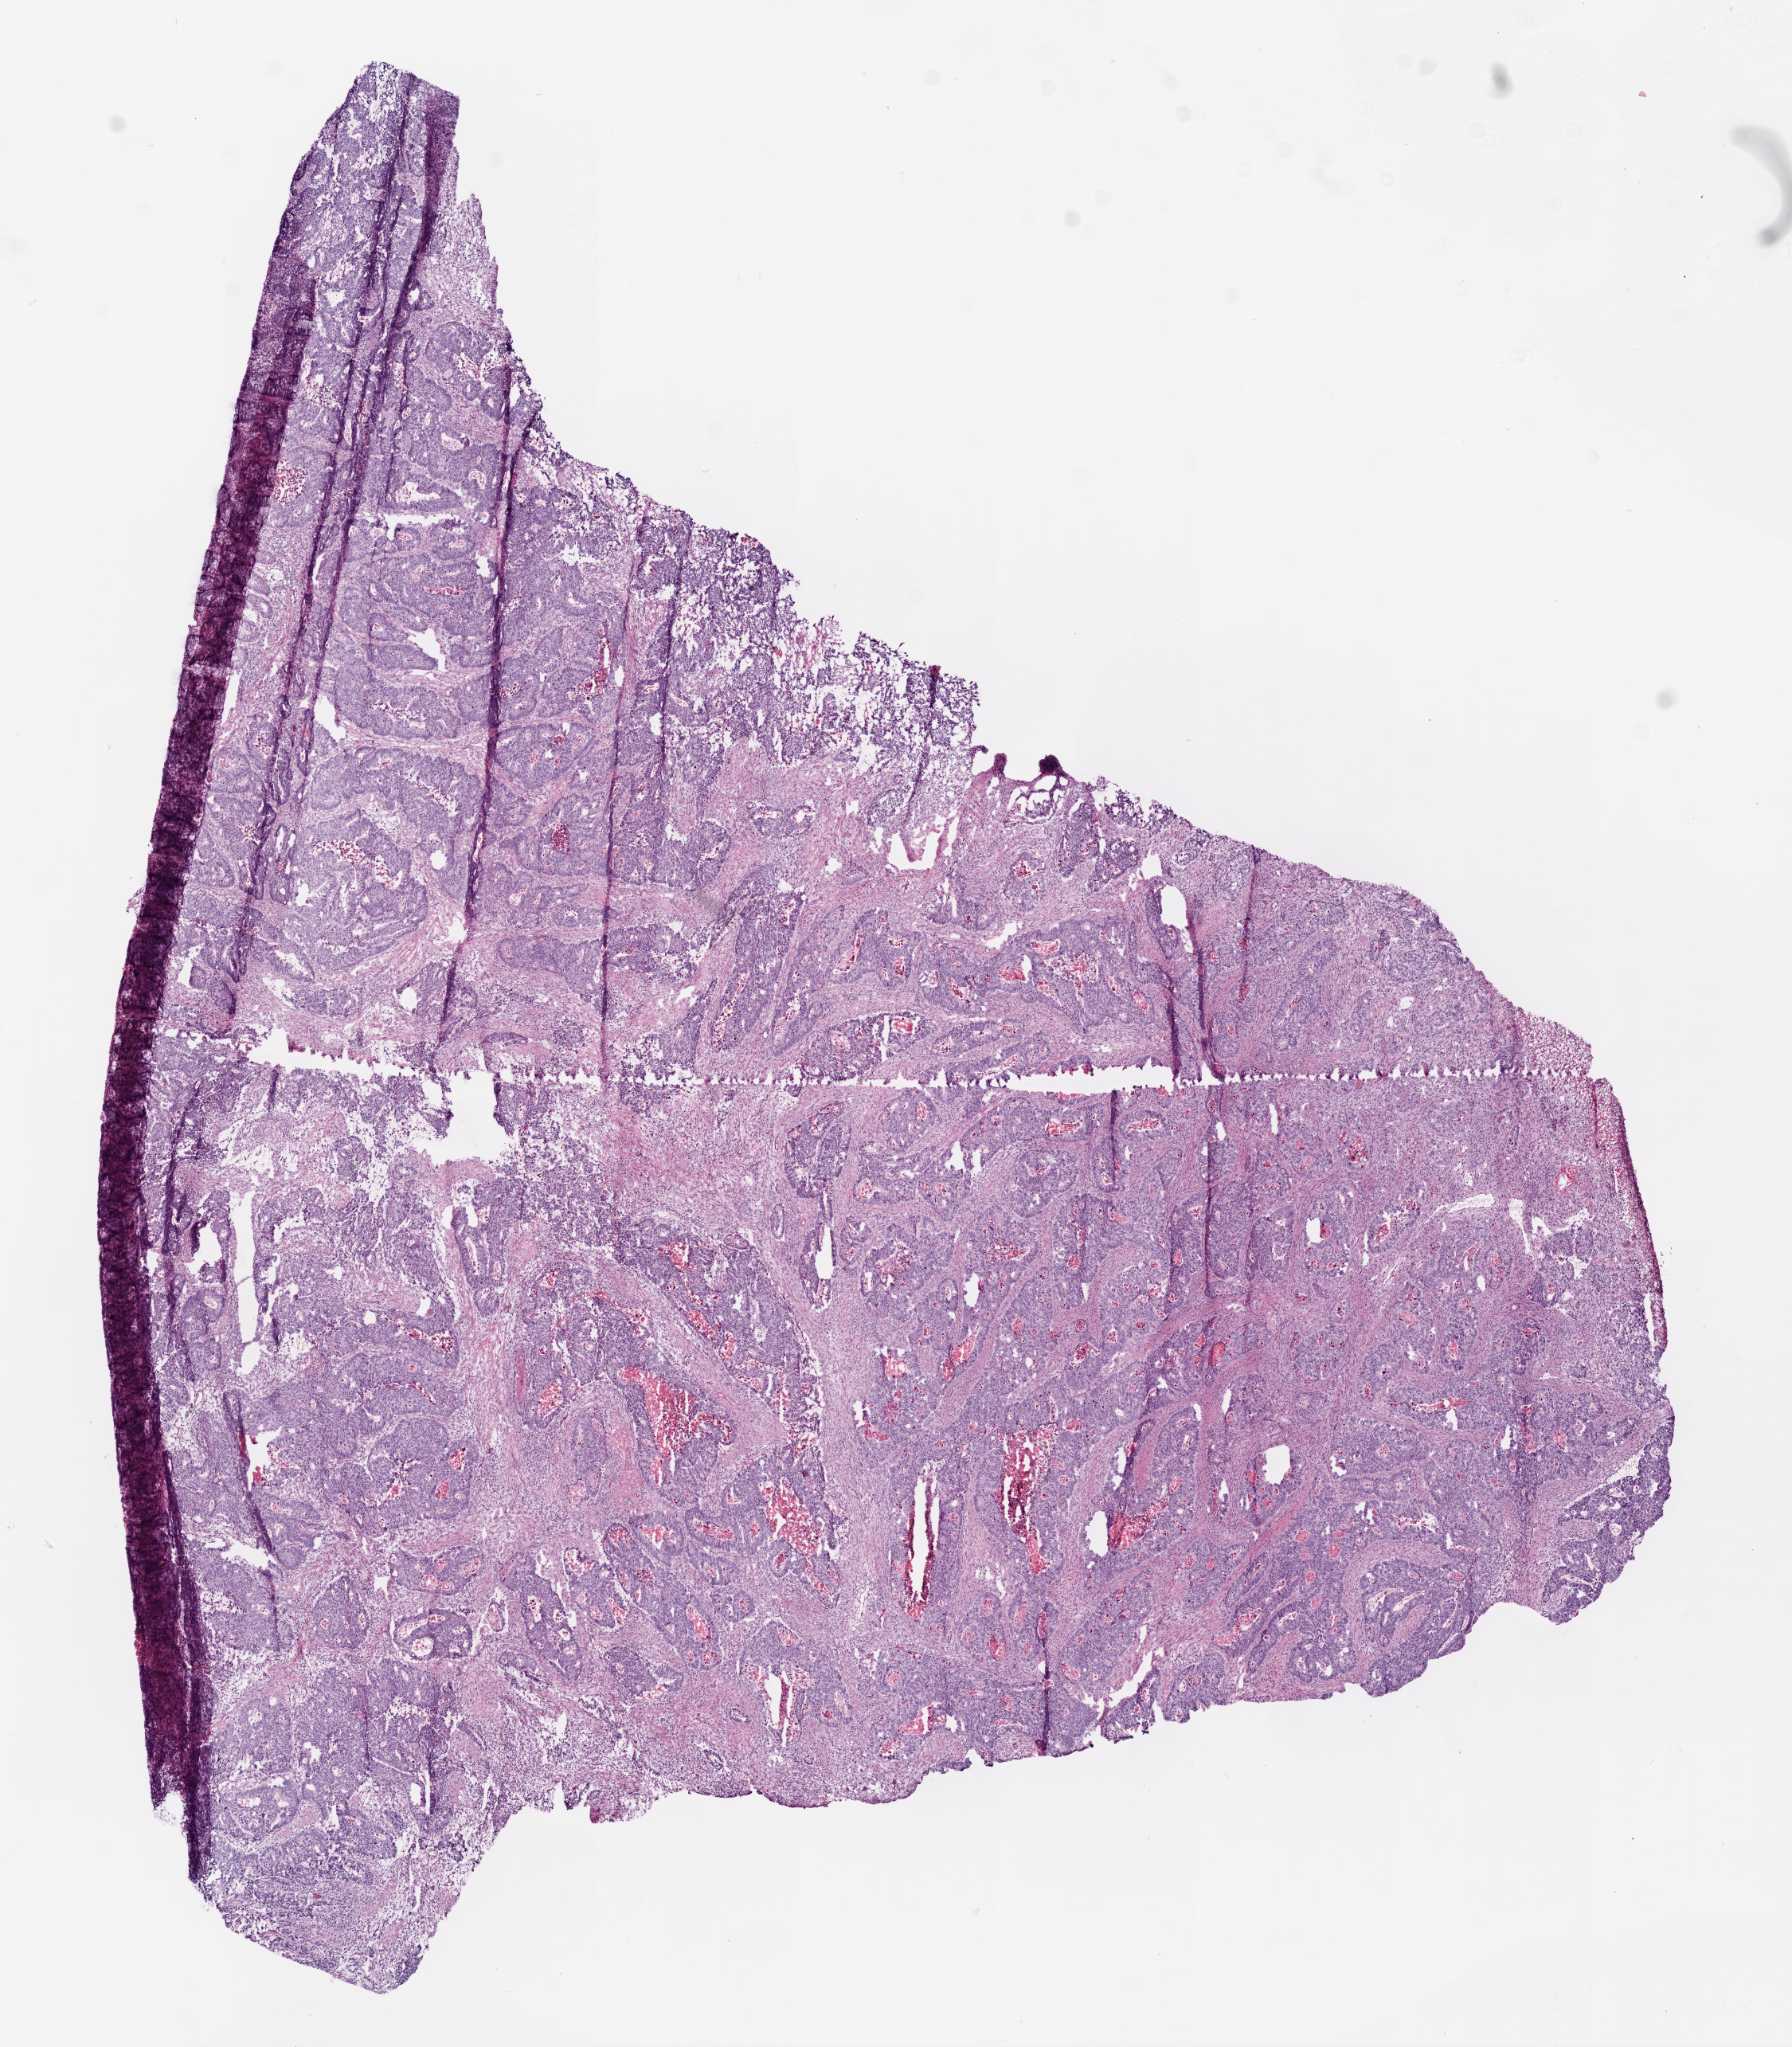
Digitized H&E tissue section (whole slide) — shown as a low-resolution overview of the whole scanned area (about 9.0 x 10.3 mm); frozen section from the bottom of the tissue portion; colon, primary tumour sample. Female patient; age at initial diagnosis 55 years. Composition of this section per pathologist review: tumour cells 95%, tumour nuclei 80%.
Histologic diagnosis: Adenocarcinoma, NOS.